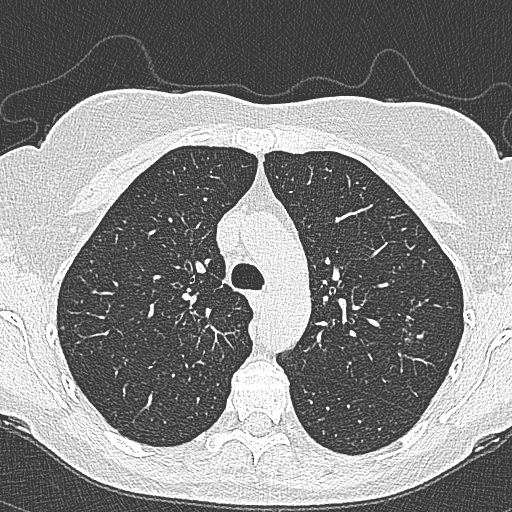
Low-dose screening chest CT, axial slice, second screening round (one year after baseline), lung window (W 1500 / L -600 HU), 1 mm slice thickness. Female participant, aged 65 years at enrolment. Current smoker at enrolment.
• Expert-annotated lung lesion, box from (x=389, y=307) to (x=434, y=352) px.
• The screening reader recorded 4 non-calcified nodules or masses ≥4 mm on this exam; which of them this box marks is not recorded.
• Official screen result: positive, change unspecified: nodule(s) >= 4 mm or enlarging nodule(s), mass(es), or other non-specific abnormalities suspicious for lung cancer.
• Later outcome: lung cancer diagnosed 54 days after this screen — bronchiolo-alveolar carcinoma, non-mucinous, left upper lobe, stage IA (AJCC 6th edition), 10 mm at pathology.